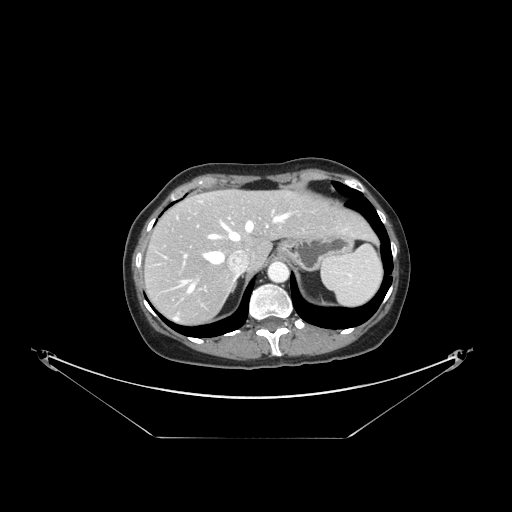
Contrast-enhanced abdominal CT, one axial slice; slice 117 of 148 in the series (ordered by position); 120 kVp; intravenous contrast given; soft-tissue window (W 400 / L 40 HU); 2.5 mm slice thickness; 512 × 512 image matrix, field of view 500 × 500 mm. Female patient, age 73 years. Case-level facts recorded for this patient, not image findings: diagnosis: colorectal cancer liver metastases, imaged before liver resection; multiple liver metastases: no; largest metastasis: 1 cm; disease in both lobes: no.
Outlined on this slice (manually delineated by an expert):
- hepatic veins: bounding box (x1, y1, x2, y2) in pixels: (181, 210, 291, 293)
- liver: (146, 191, 373, 323)
- planned liver remnant (the part of the liver to remain after resection): (171, 191, 372, 266)
- portal vein (with intrahepatic branches): (184, 254, 187, 258)